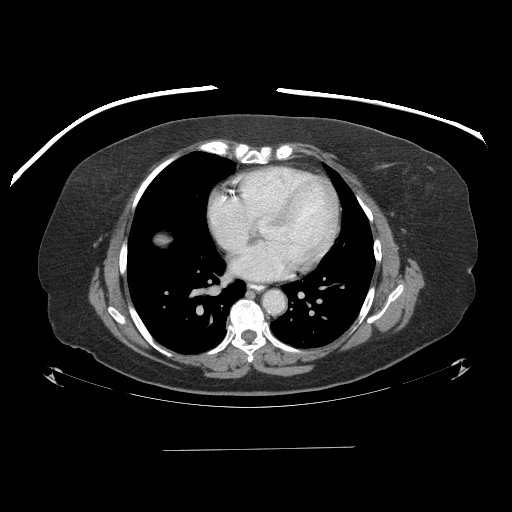
Contrast-enhanced abdominal CT (liver protocol), one axial slice; slice 91 of 103 in the series (ordered by position); reconstruction kernel STANDARD; 120 kVp; one of 2 acquisitions stored at this slice position; soft-tissue window (W 400 / L 40 HU); 2.5 mm slice thickness; 512 × 512 image matrix. From the clinical record (not read from this slice): diagnosis: hepatocellular carcinoma (patient treated with transarterial chemoembolisation; whether this scan precedes or follows treatment is not stated here); TNM stage (as recorded): Stage-IIIA; Child-Pugh class: A; tumour differentiation: poorly differentiated; tumour nodularity: multinodular.
Annotated regions visible in this slice (semi-automatic segmentation, software-assisted and operator-edited):
- liver parenchyma outside the tumour (the mass and vessels are separate outlines, so this box may not span the whole liver): bounding box (x1, y1, x2, y2) in pixels: (156, 234, 170, 244)